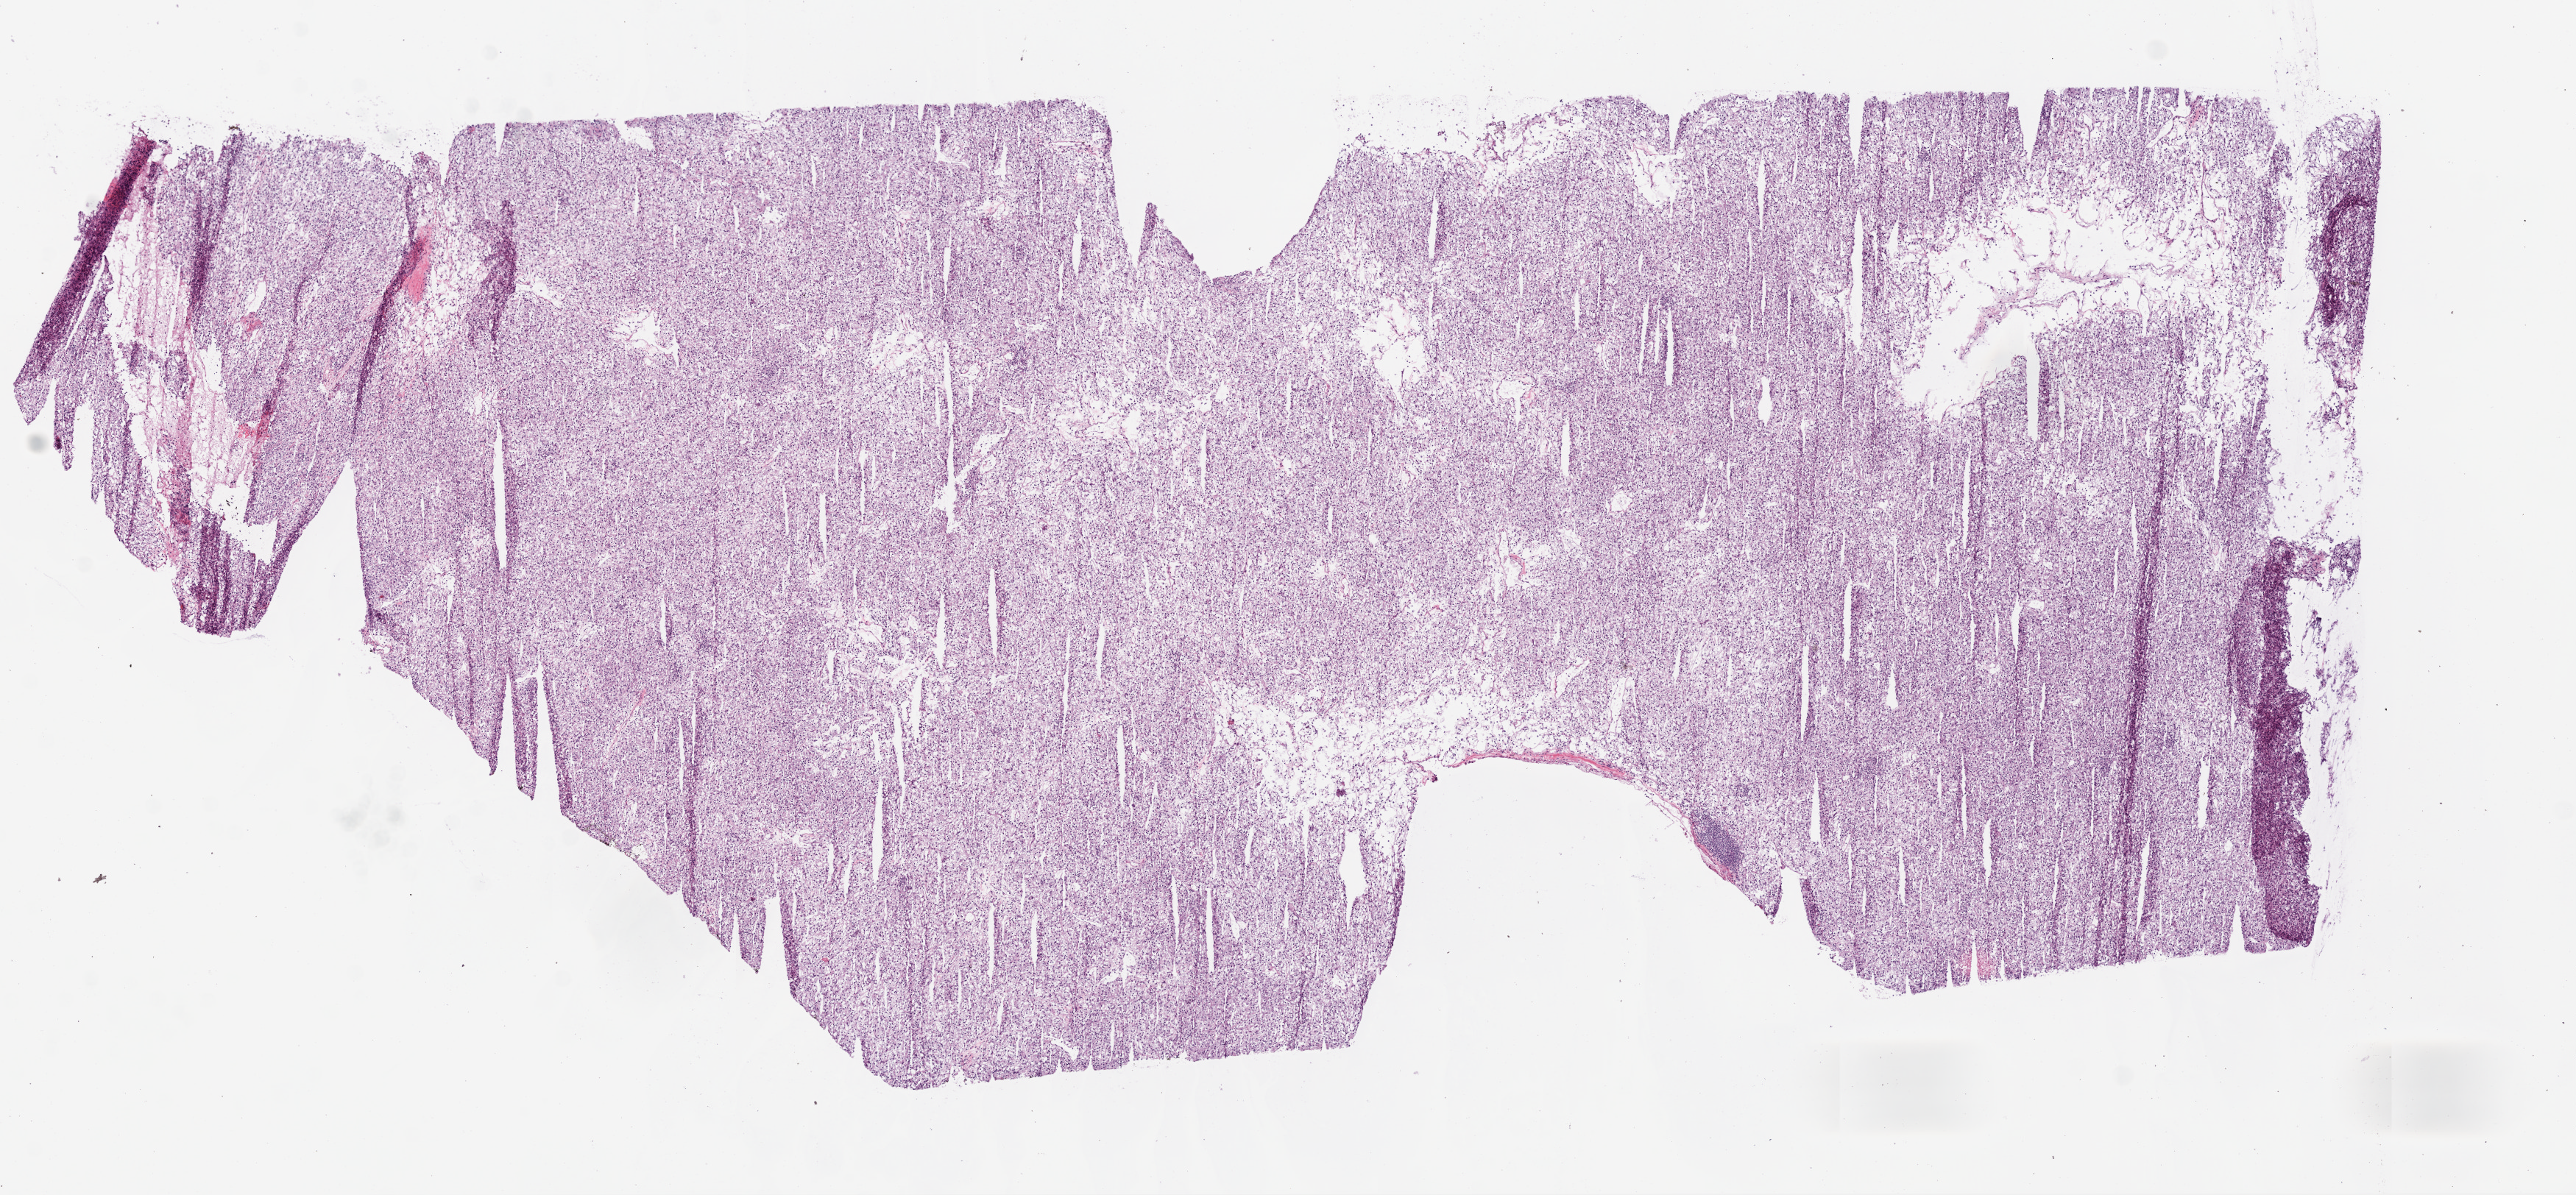
H&E whole-slide image, low-resolution overview of the scanned area, about 14.0 x 6.5 mm (from a 20x scan). Frozen section from the top of the tissue portion. Primary tumour sample from the kidney. Male patient; age at initial diagnosis 61 years. Histologic grade: G2 (moderately differentiated). Slide review estimates, as recorded: tumour cells 100%, tumour nuclei 99%, normal cells 0%, stromal cells 0%, necrosis 0%. Infiltration values recorded for this section: lymphocyte infiltration 1%.
- diagnosis: Clear cell adenocarcinoma, NOS
- AJCC pathologic stage: I
- TNM: T1b NX M0